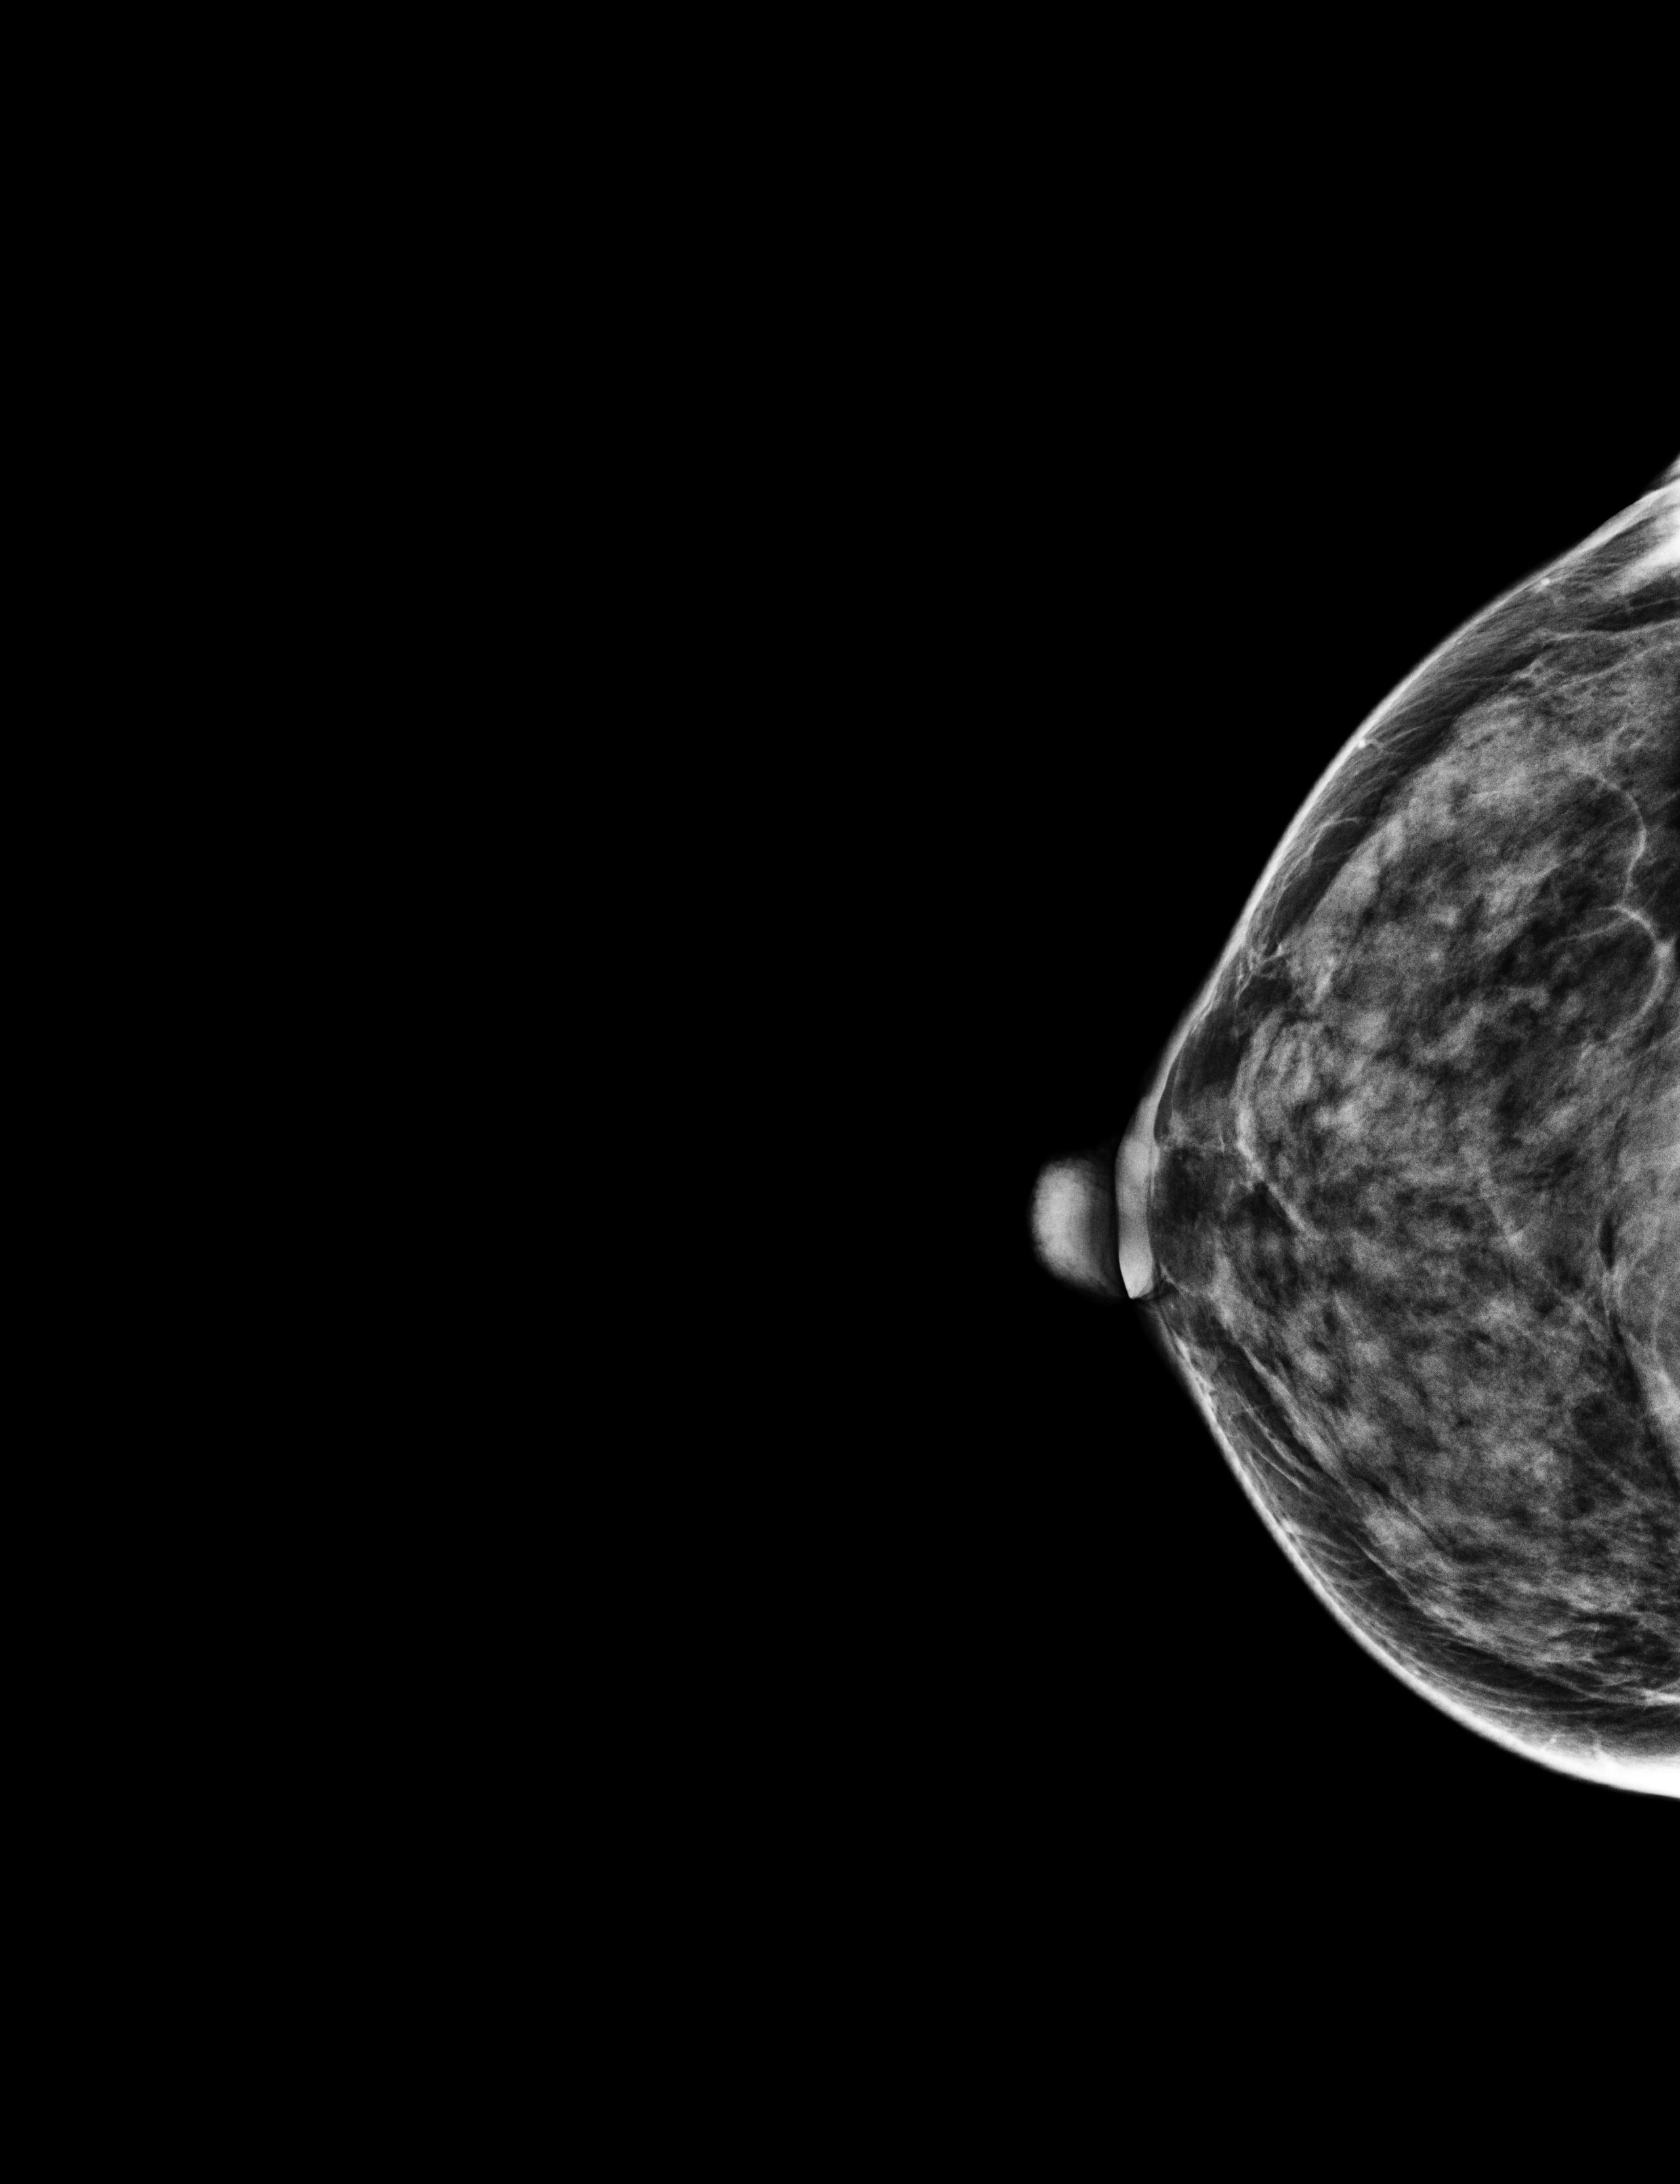
Full-field digital mammogram (FFDM); right breast; cranio-caudal projection; screening examination. Patient aged 42 years (female).
- BI-RADS breast density category at the screening exam (both breasts, scale 1–4): 3
- final BI-RADS assessment for this screening round (tomosynthesis exam, both breasts): category 1
- recall: no recall after this screen